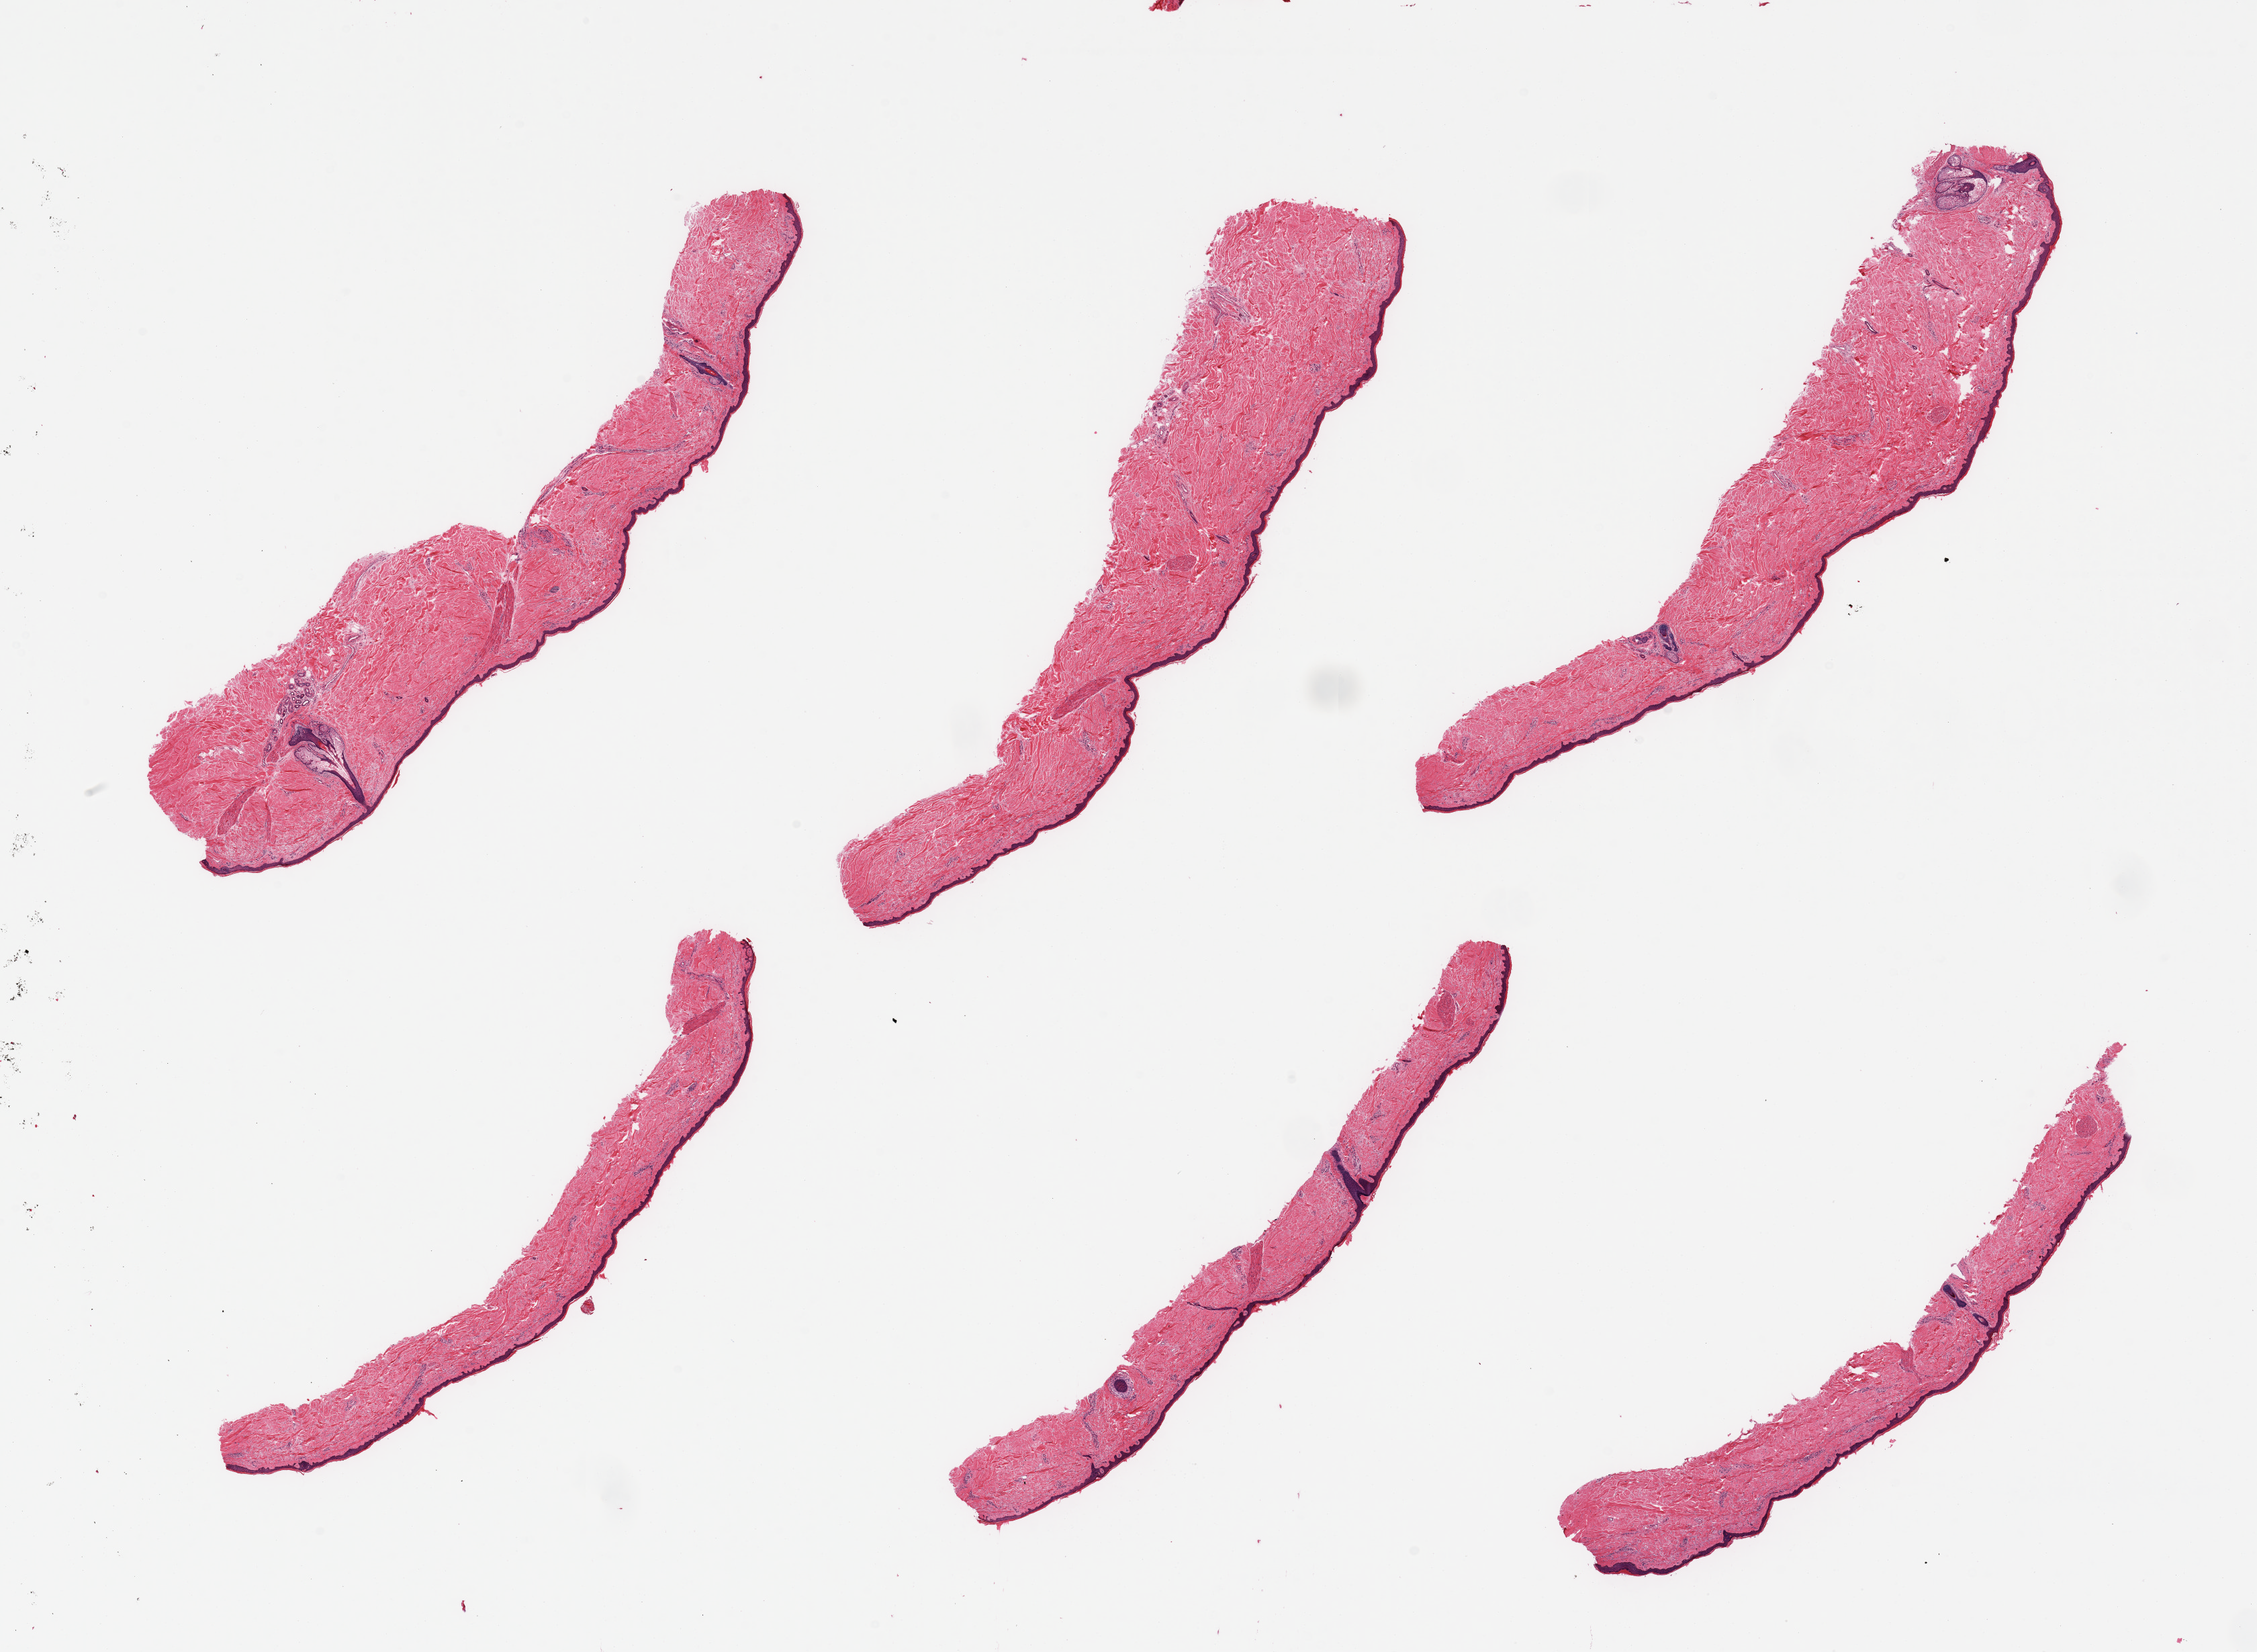
Digitized hematoxylin and eosin (H&E)-stained section, shown as a low-resolution overview of the whole scanned area (about 26.6 x 19.5 mm, from a 20x scan). PAXgene-fixed, paraffin-embedded tissue. Section of skin of lower leg (target tissue). Tissue donor sample.
- review note (as recorded): 6 pieces, no dermal fat; squamous epithelium is ~45-60 microns